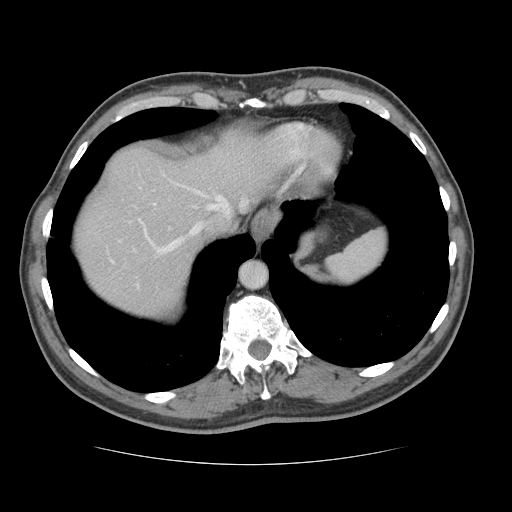
Contrast-enhanced abdominal CT, one axial slice. Slice 112 of 134 in the series (ordered by position). Reconstruction kernel STANDARD. 120 kVp. Intravenous contrast given. Soft-tissue window (W 400 / L 40 HU). 2.5 mm slice thickness. 512 × 512 image matrix, field of view 377 × 377 mm. Male patient, age 68 years. Case-level facts recorded for this patient, not image findings: diagnosis: colorectal cancer liver metastases, imaged before liver resection; multiple liver metastases: yes; largest metastasis: 2.2 cm.
Annotated regions visible in this slice (expert manual segmentation):
- hepatic veins: box from (x=111, y=172) to (x=246, y=262) px
- liver: (x=76, y=144)–(x=263, y=314)
- planned liver remnant (the part of the liver to remain after resection): (x=76, y=144)–(x=264, y=305)